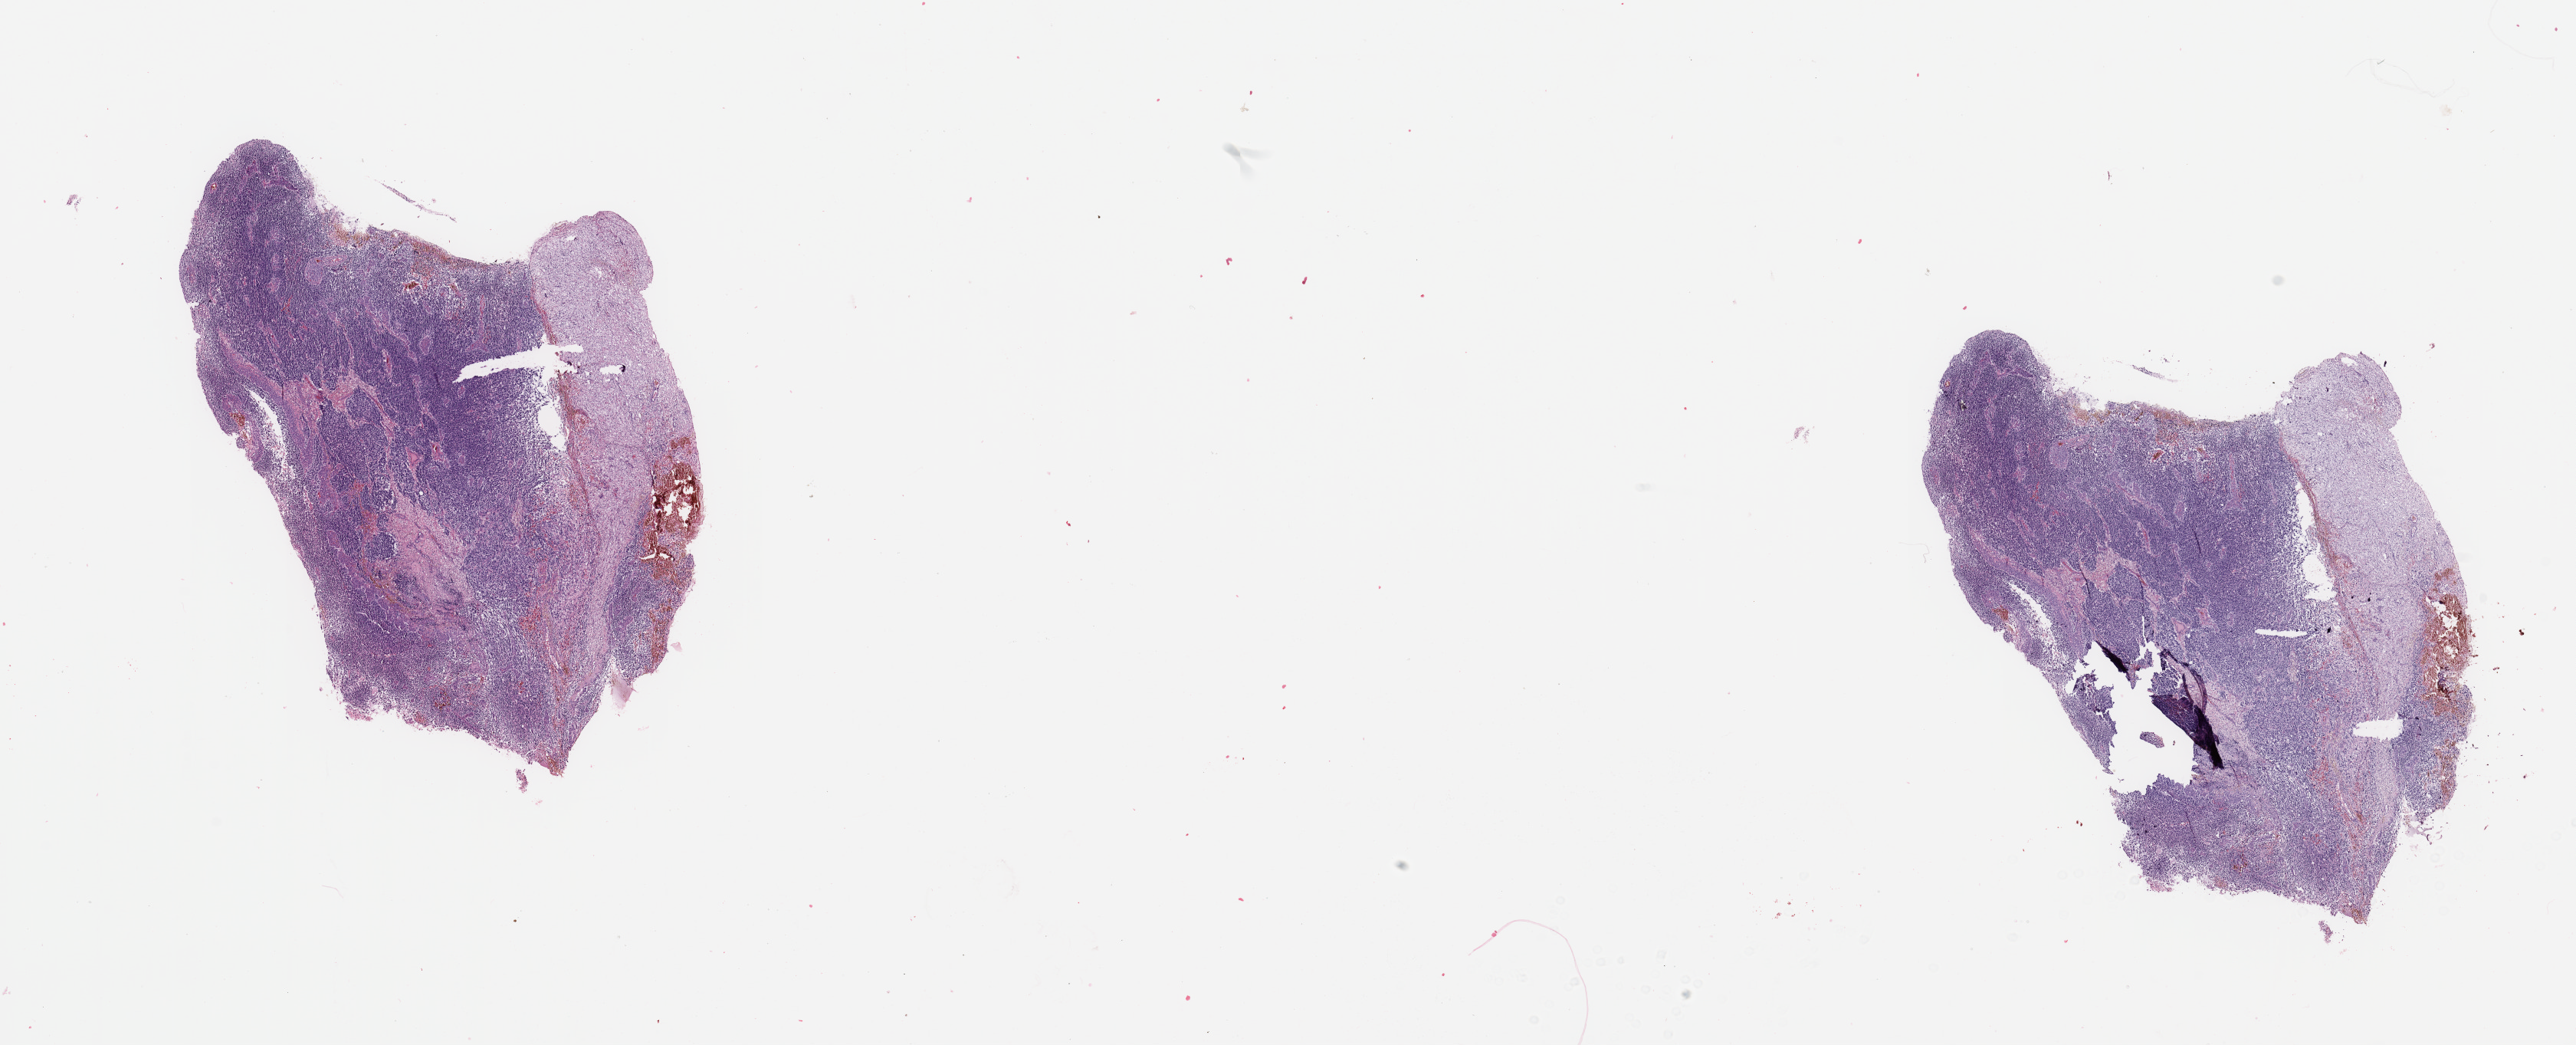
Hematoxylin and eosin (H&E) stained whole-slide image, a low-resolution overview of the entire scanned area, about 26.6 x 10.8 mm (from a 20x scan); brain, tumour tissue. Patient: female, age 60 years.
Histologic diagnosis: Glioblastoma.